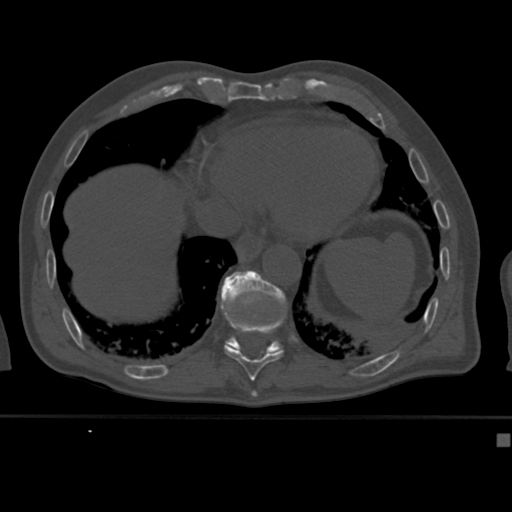
CT including the spine, one axial slice; slice 223 of 430 in the series (ordered by position); reconstruction kernel Br40s; 120 kVp; bone window (W 1800 / L 400 HU); 1.5 mm slice thickness; 512 × 512 image matrix. Patient: male, 64 years. Case-level facts recorded for this patient, not image findings: primary cancer: uterus.
Annotated regions visible in this slice (semi-automatic segmentation, software-assisted and operator-edited):
- T10 vertebra: box from (x=224, y=314) to (x=284, y=382) px
- T11 vertebra: (x=221, y=271)–(x=287, y=354)